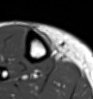
MRI of an extremity soft-tissue mass, one axial slice. Position 11 of 54 along the scan axis. MR volume resampled by the dataset authors to the PET/CT grid (not the native acquisition matrix). 93 × 99 image matrix. Female patient. From the clinical record (not read from this slice): histological type: undifferentiated – high grade; grade: high; site of the primary tumour: right thigh.
Structures marked on this image (expert contour drawn on MRI and transferred to this co-registered scan by the dataset authors):
- gross tumour volume (mass): bounding box [x1, y1, x2, y2] px = [38, 32, 49, 44]